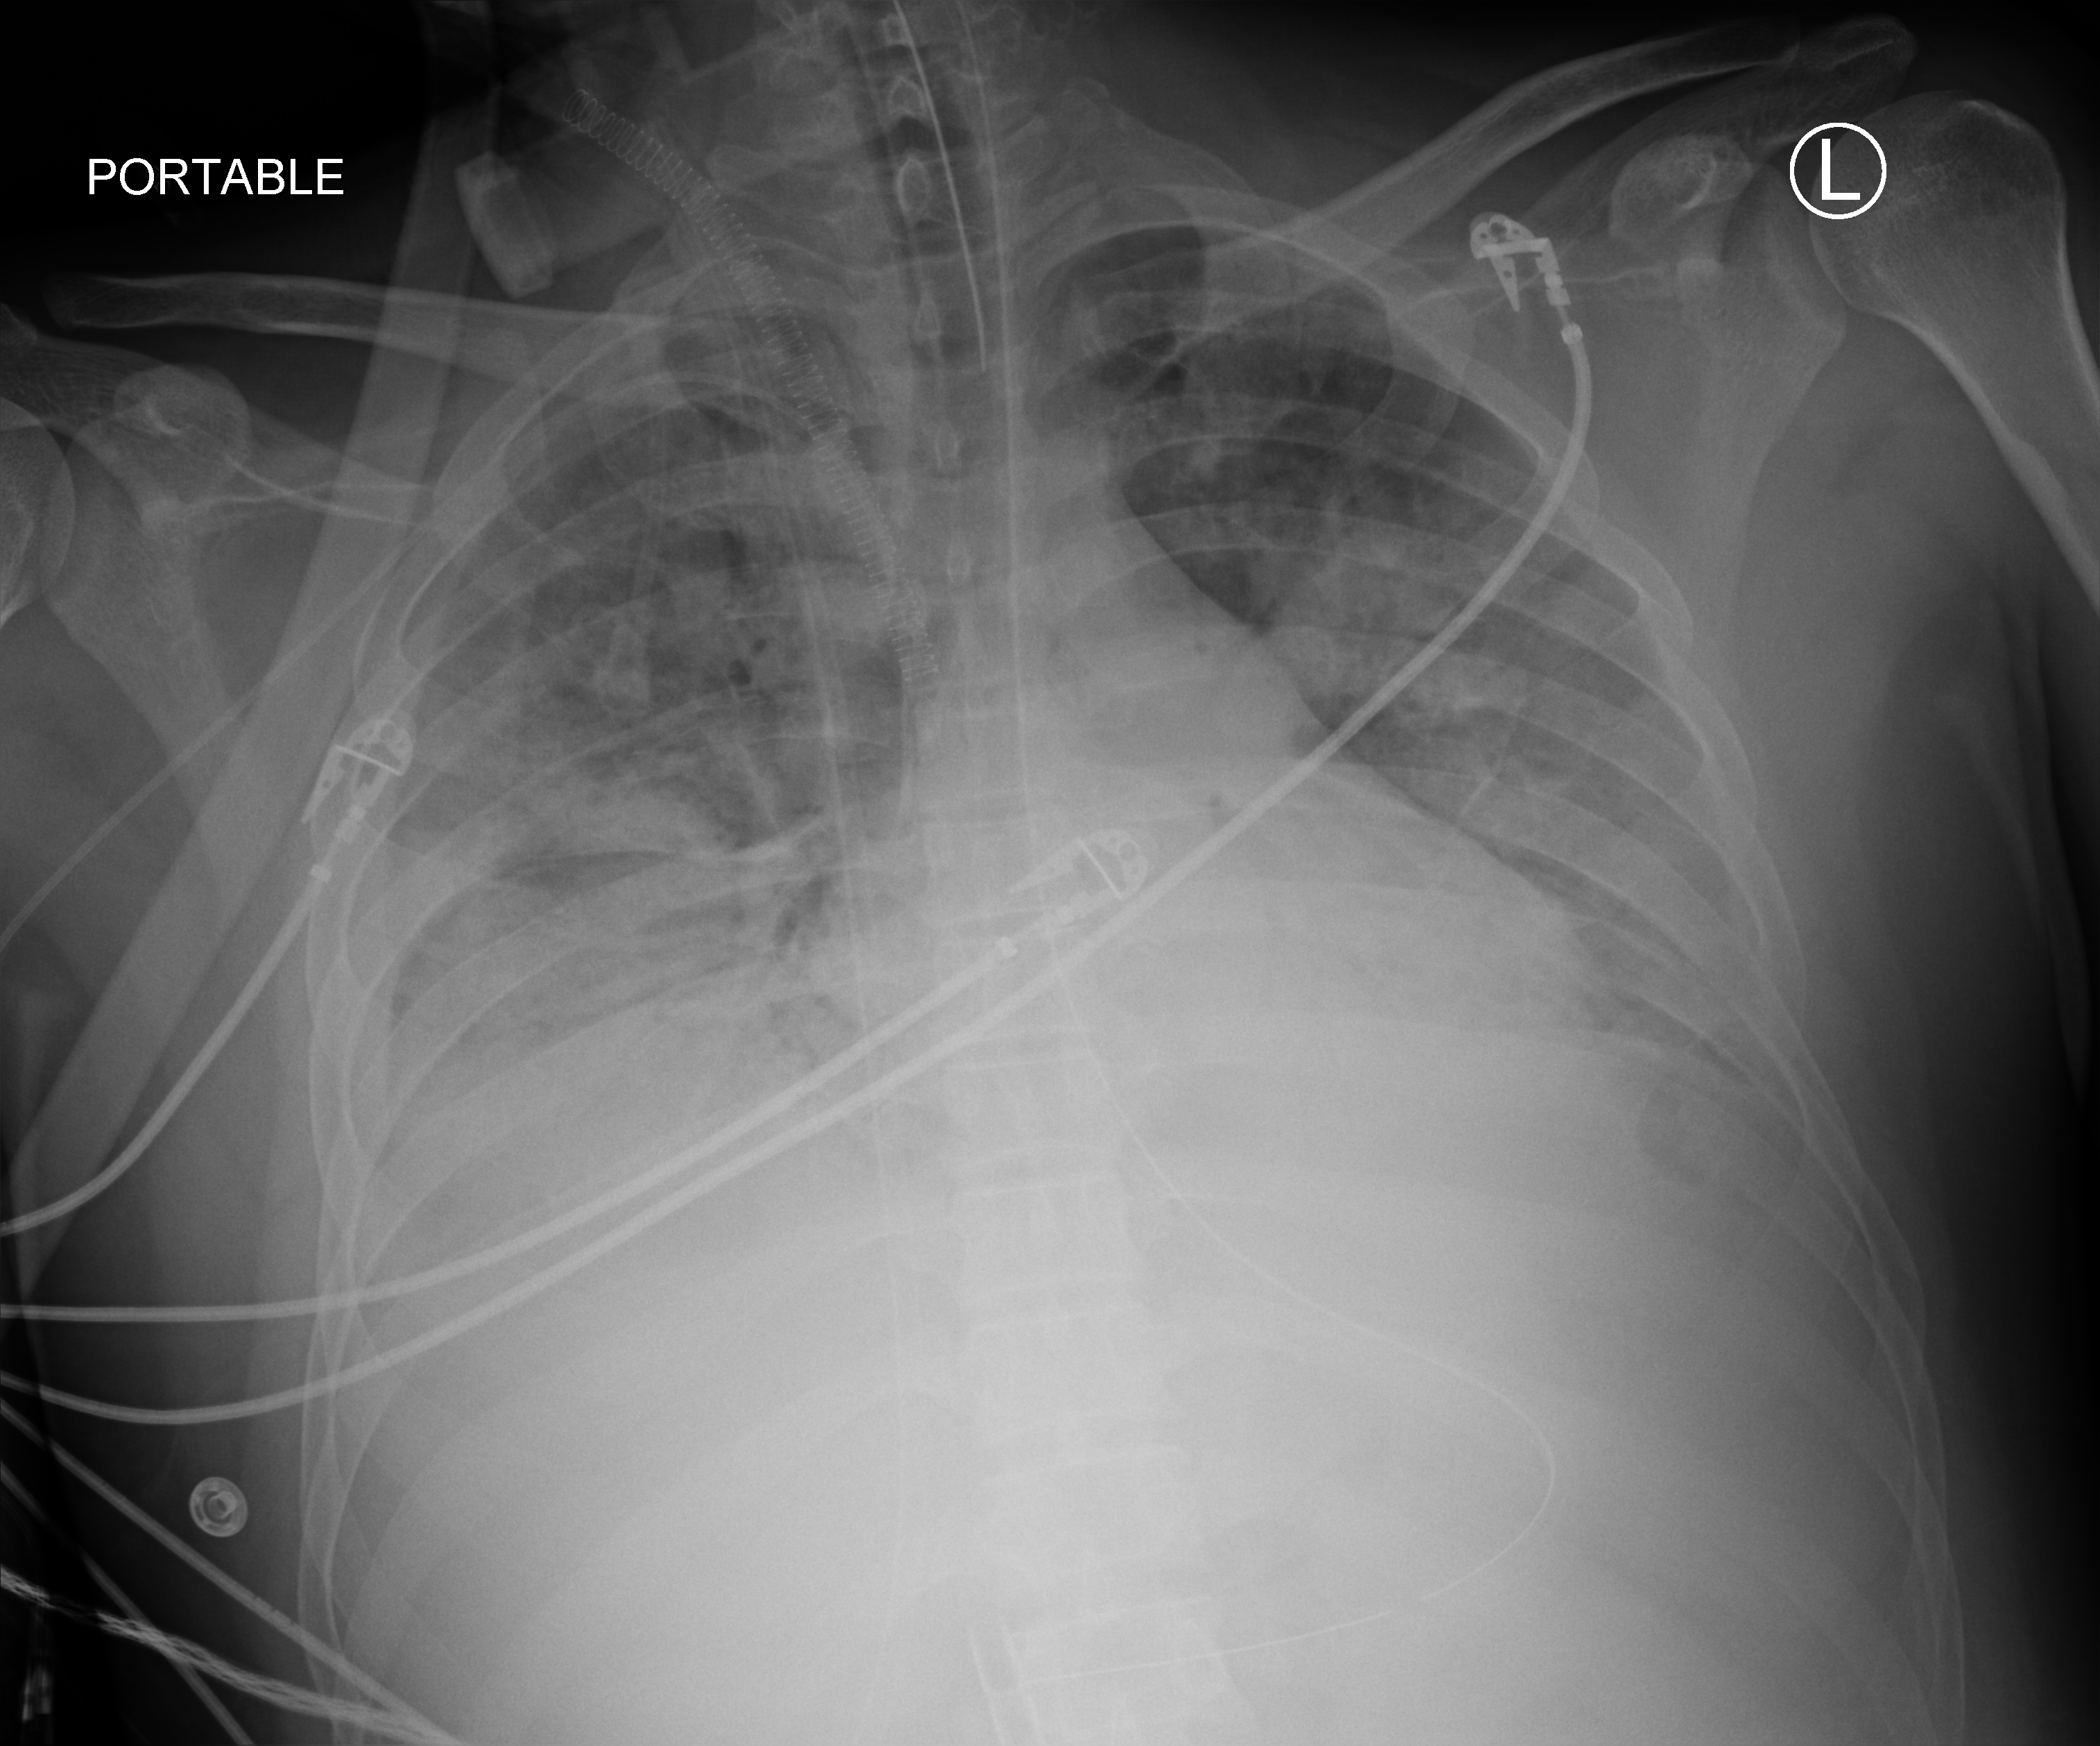
Bedside chest radiograph (computed radiography). Adult patient hospitalised with COVID-19, age 18–59 years.
From the hospital-stay record, not from the radiograph (when in the stay this image was taken is not recorded): admitted to intensive care during this hospital stay: yes; COPD (admission record): no.